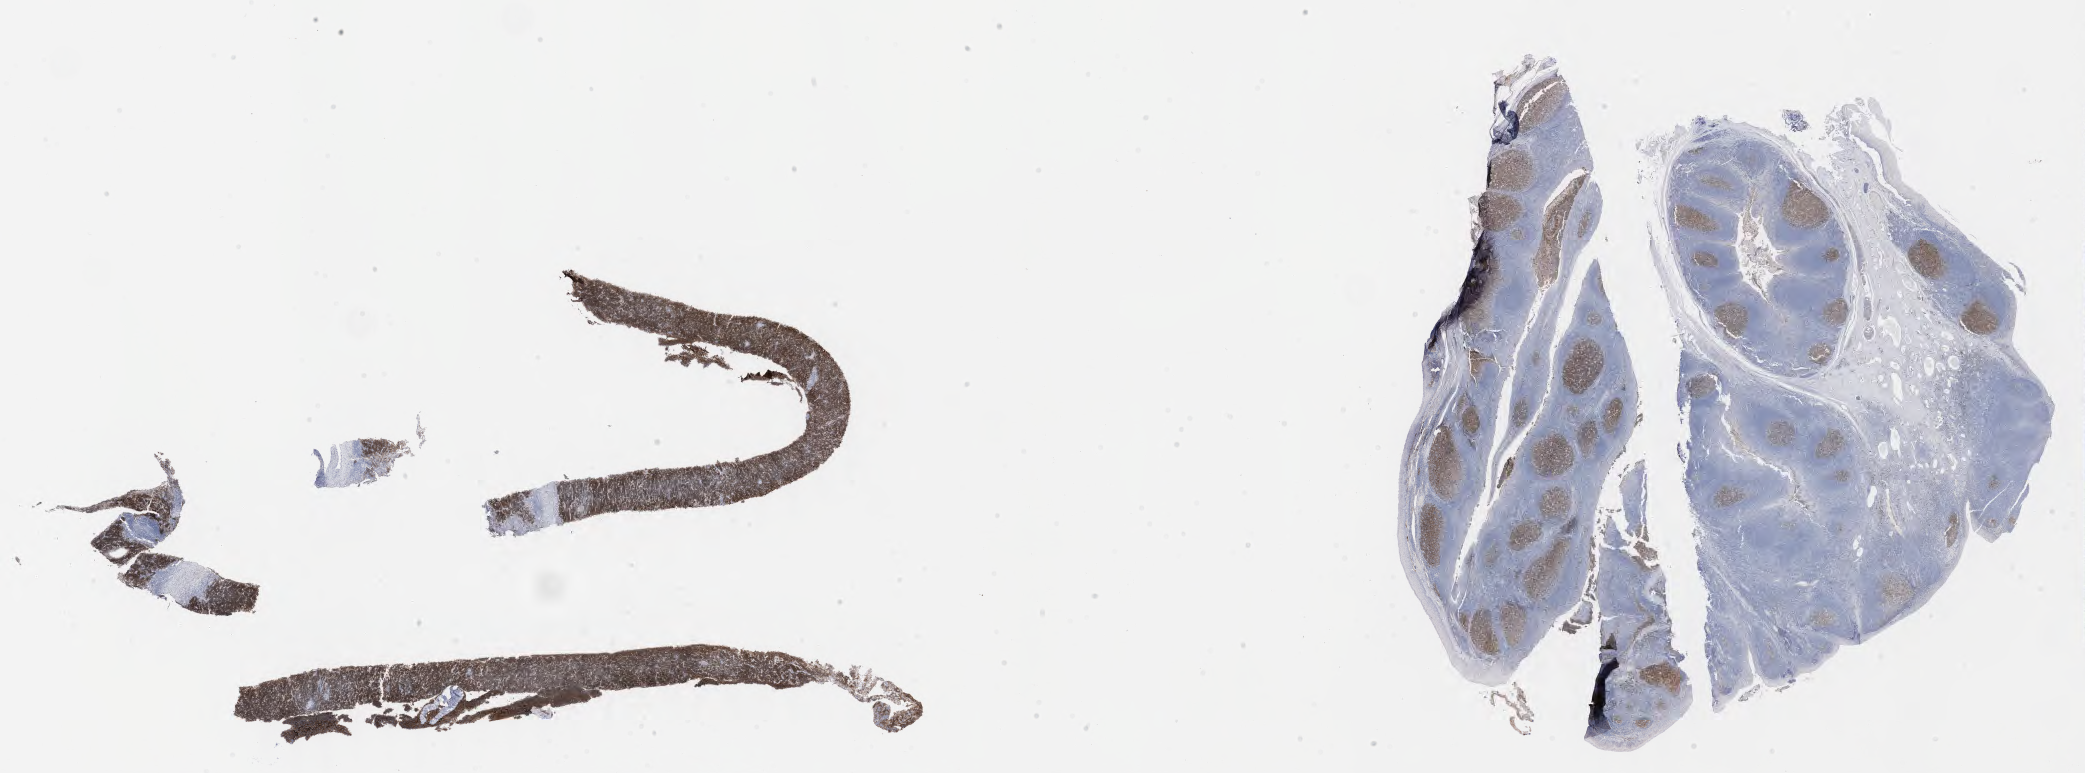
IHC for CD10, whole-slide image, whole scanned area (about 33.7 x 12.5 mm) shown as a low-resolution overview, specimen: tumor tissue. Male patient, 55 years old.
Diagnosis: Burkitt lymphoma, NOS.